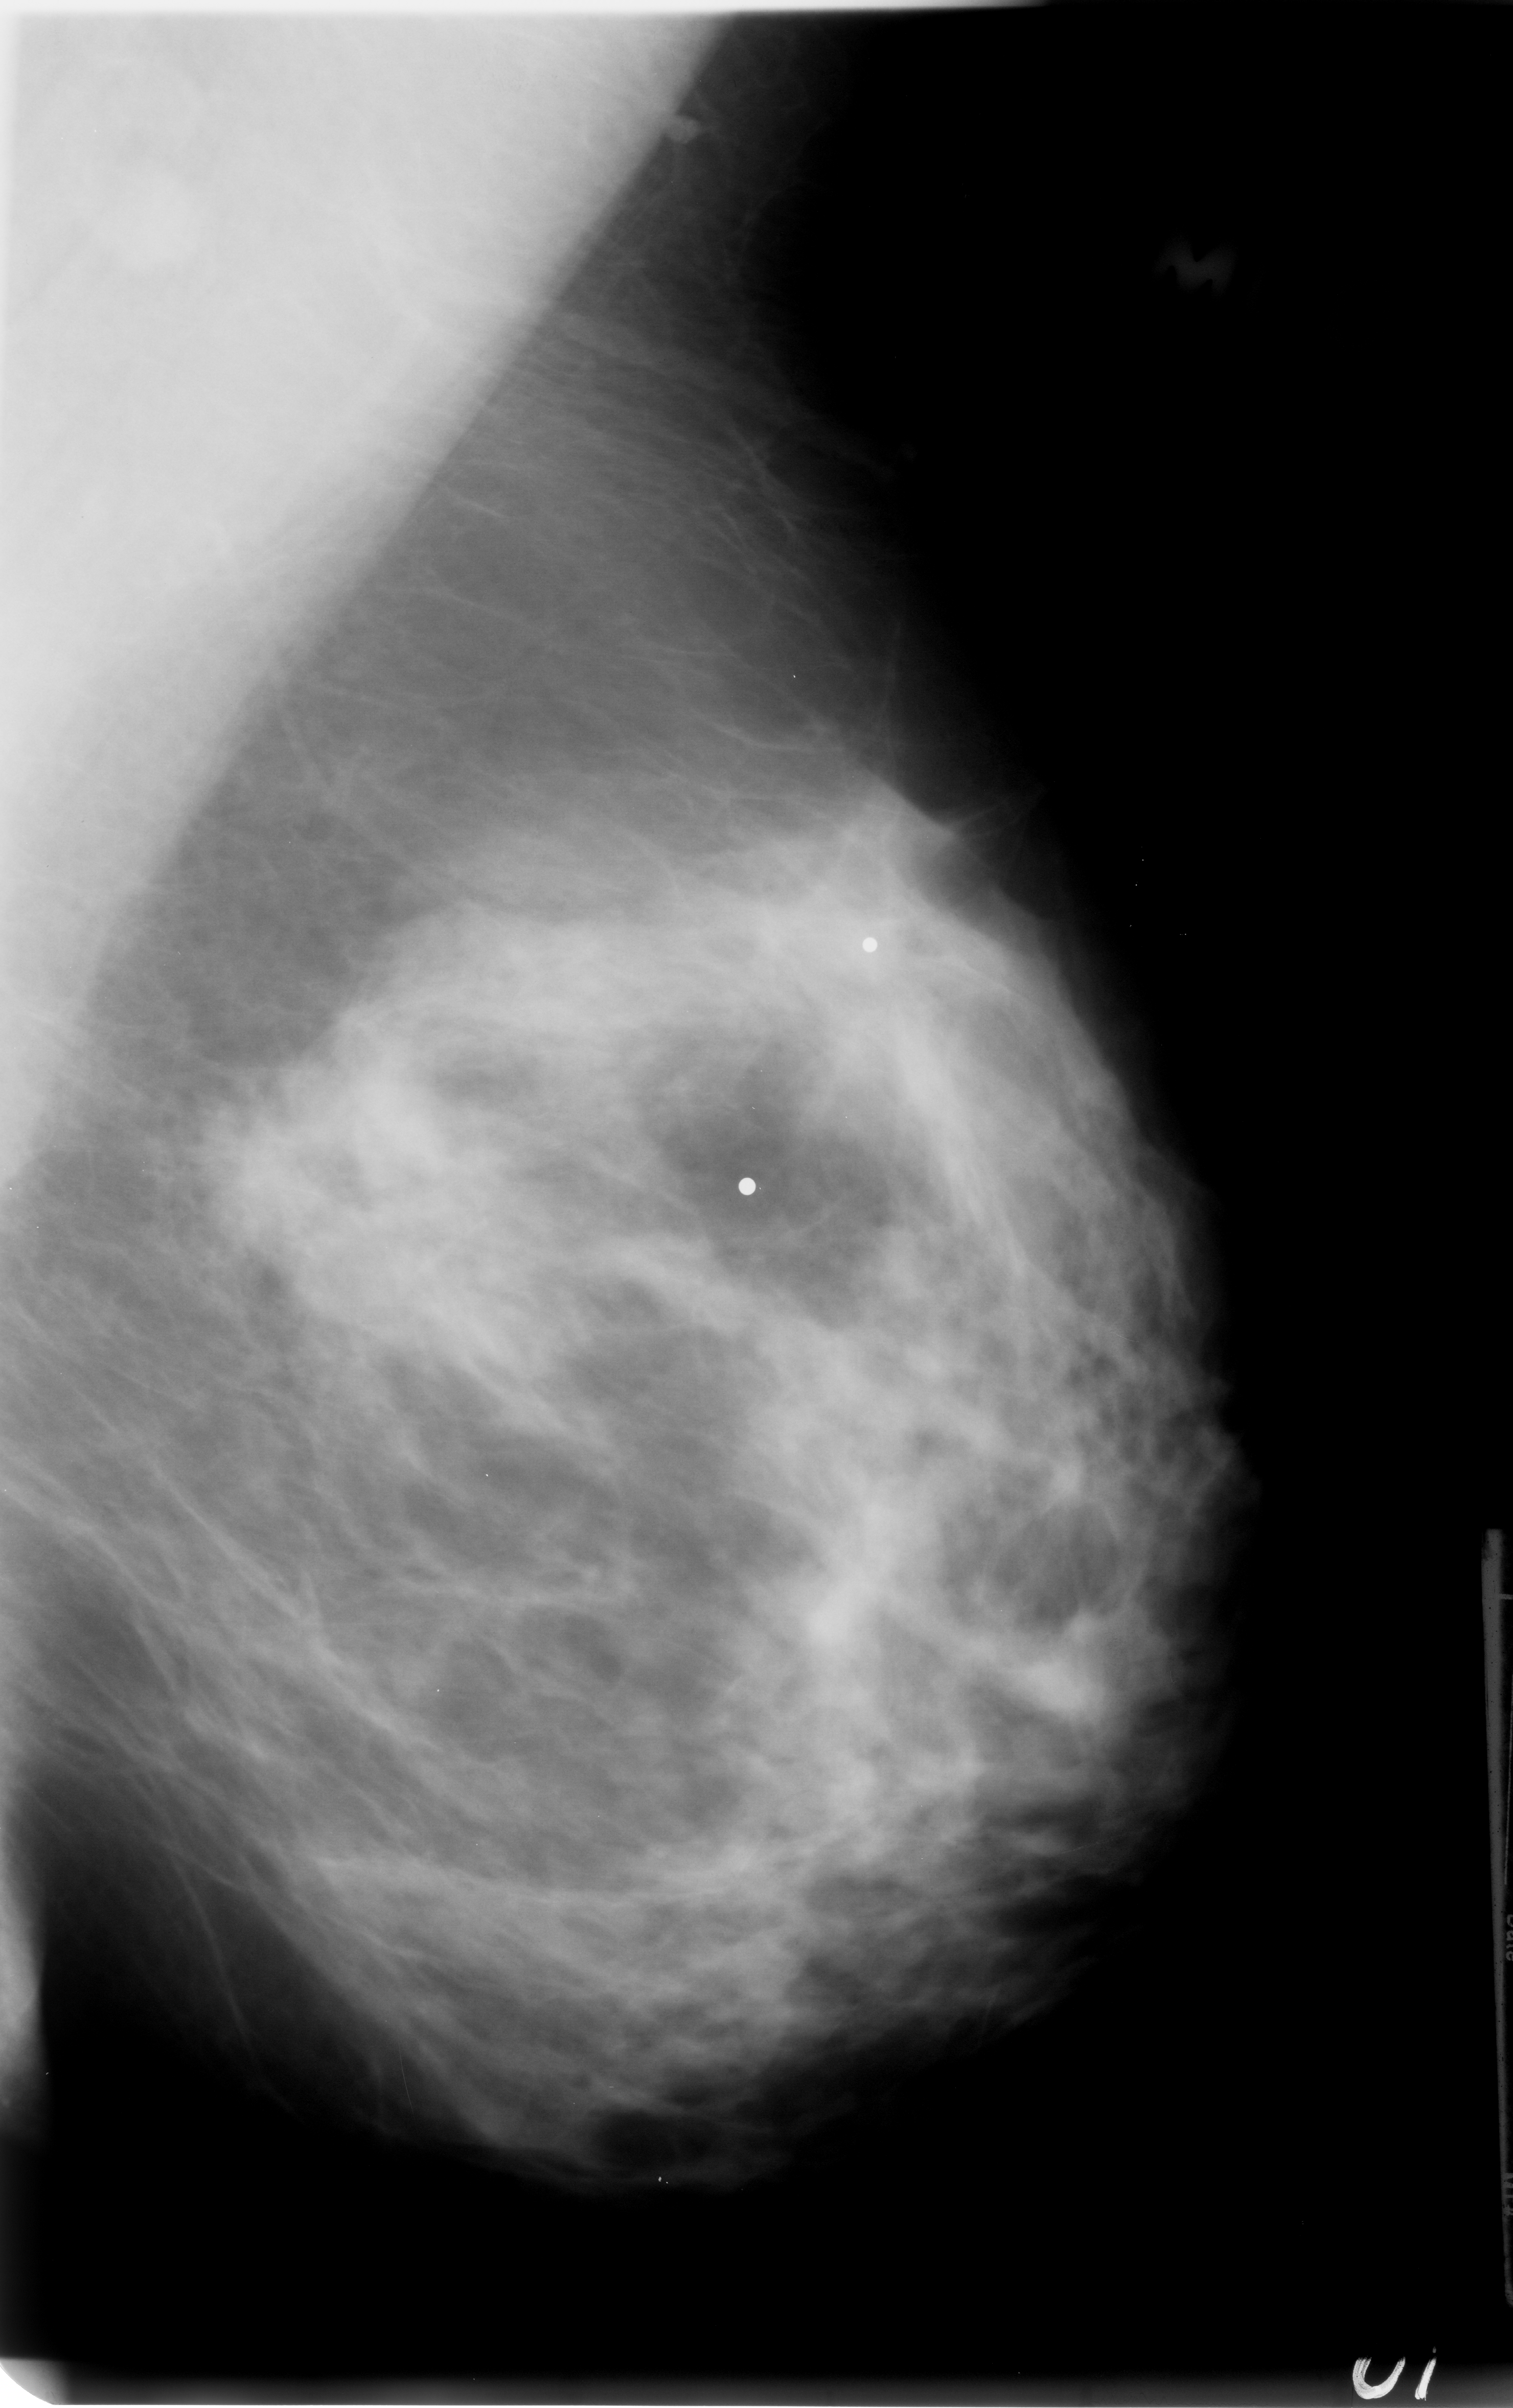
Digitized screen-film mammogram; left breast; MLO view; breast composition: heterogeneously dense (BI-RADS density category 3 of 4).
Marked abnormality: mass, shape irregular, margins ill defined; BI-RADS assessment category 4; subtlety rating 2 on a 1 (subtle) to 5 (obvious) scale; pathology (as recorded): malignant.